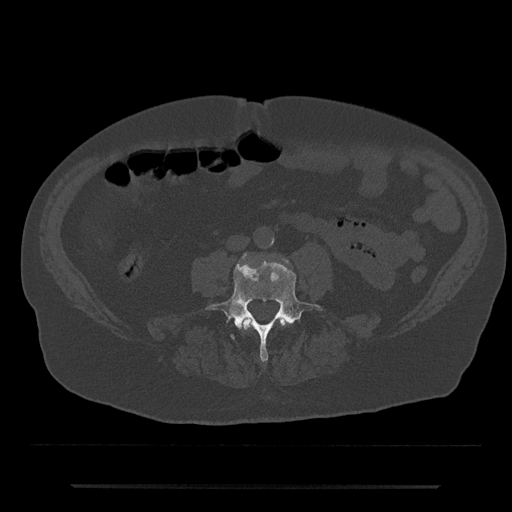
CT including the spine, one axial slice; position 359 of 797 along the scan axis; 120 kVp; bone window (W 1800 / L 400 HU); 512 × 512 image matrix, field of view 434 × 434 mm. Male patient, age 80 years. Case-level facts recorded for this patient, not image findings: primary cancer: prostate.
Structures marked on this image (semi-automatically segmented with operator editing):
- L3 vertebra: bounding box <241,318,290,330> (left, top, right, bottom; pixels)
- L4 vertebra: <206,253,322,362>